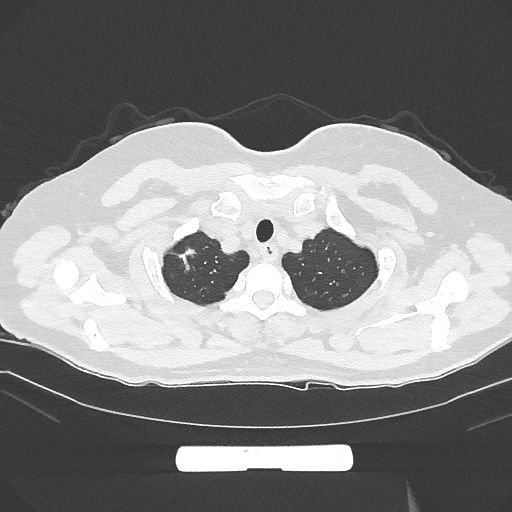
Chest CT, one axial slice. 120 kVp. Lung window (W 1500 / L -600 HU). 1 mm slice thickness. 512 × 512 image matrix, field of view 369 × 369 mm. Patient: female, 58 years. From the clinical record (not read from this slice): clinical TNM (as recorded): T1b N0 M0; histopathological grade: G2-3.
Annotated regions visible in this slice (bounding box drawn by a radiologist):
- lung tumour (recorded histology: adenocarcinoma): bounding box [x1, y1, x2, y2] px = [169, 239, 201, 276]